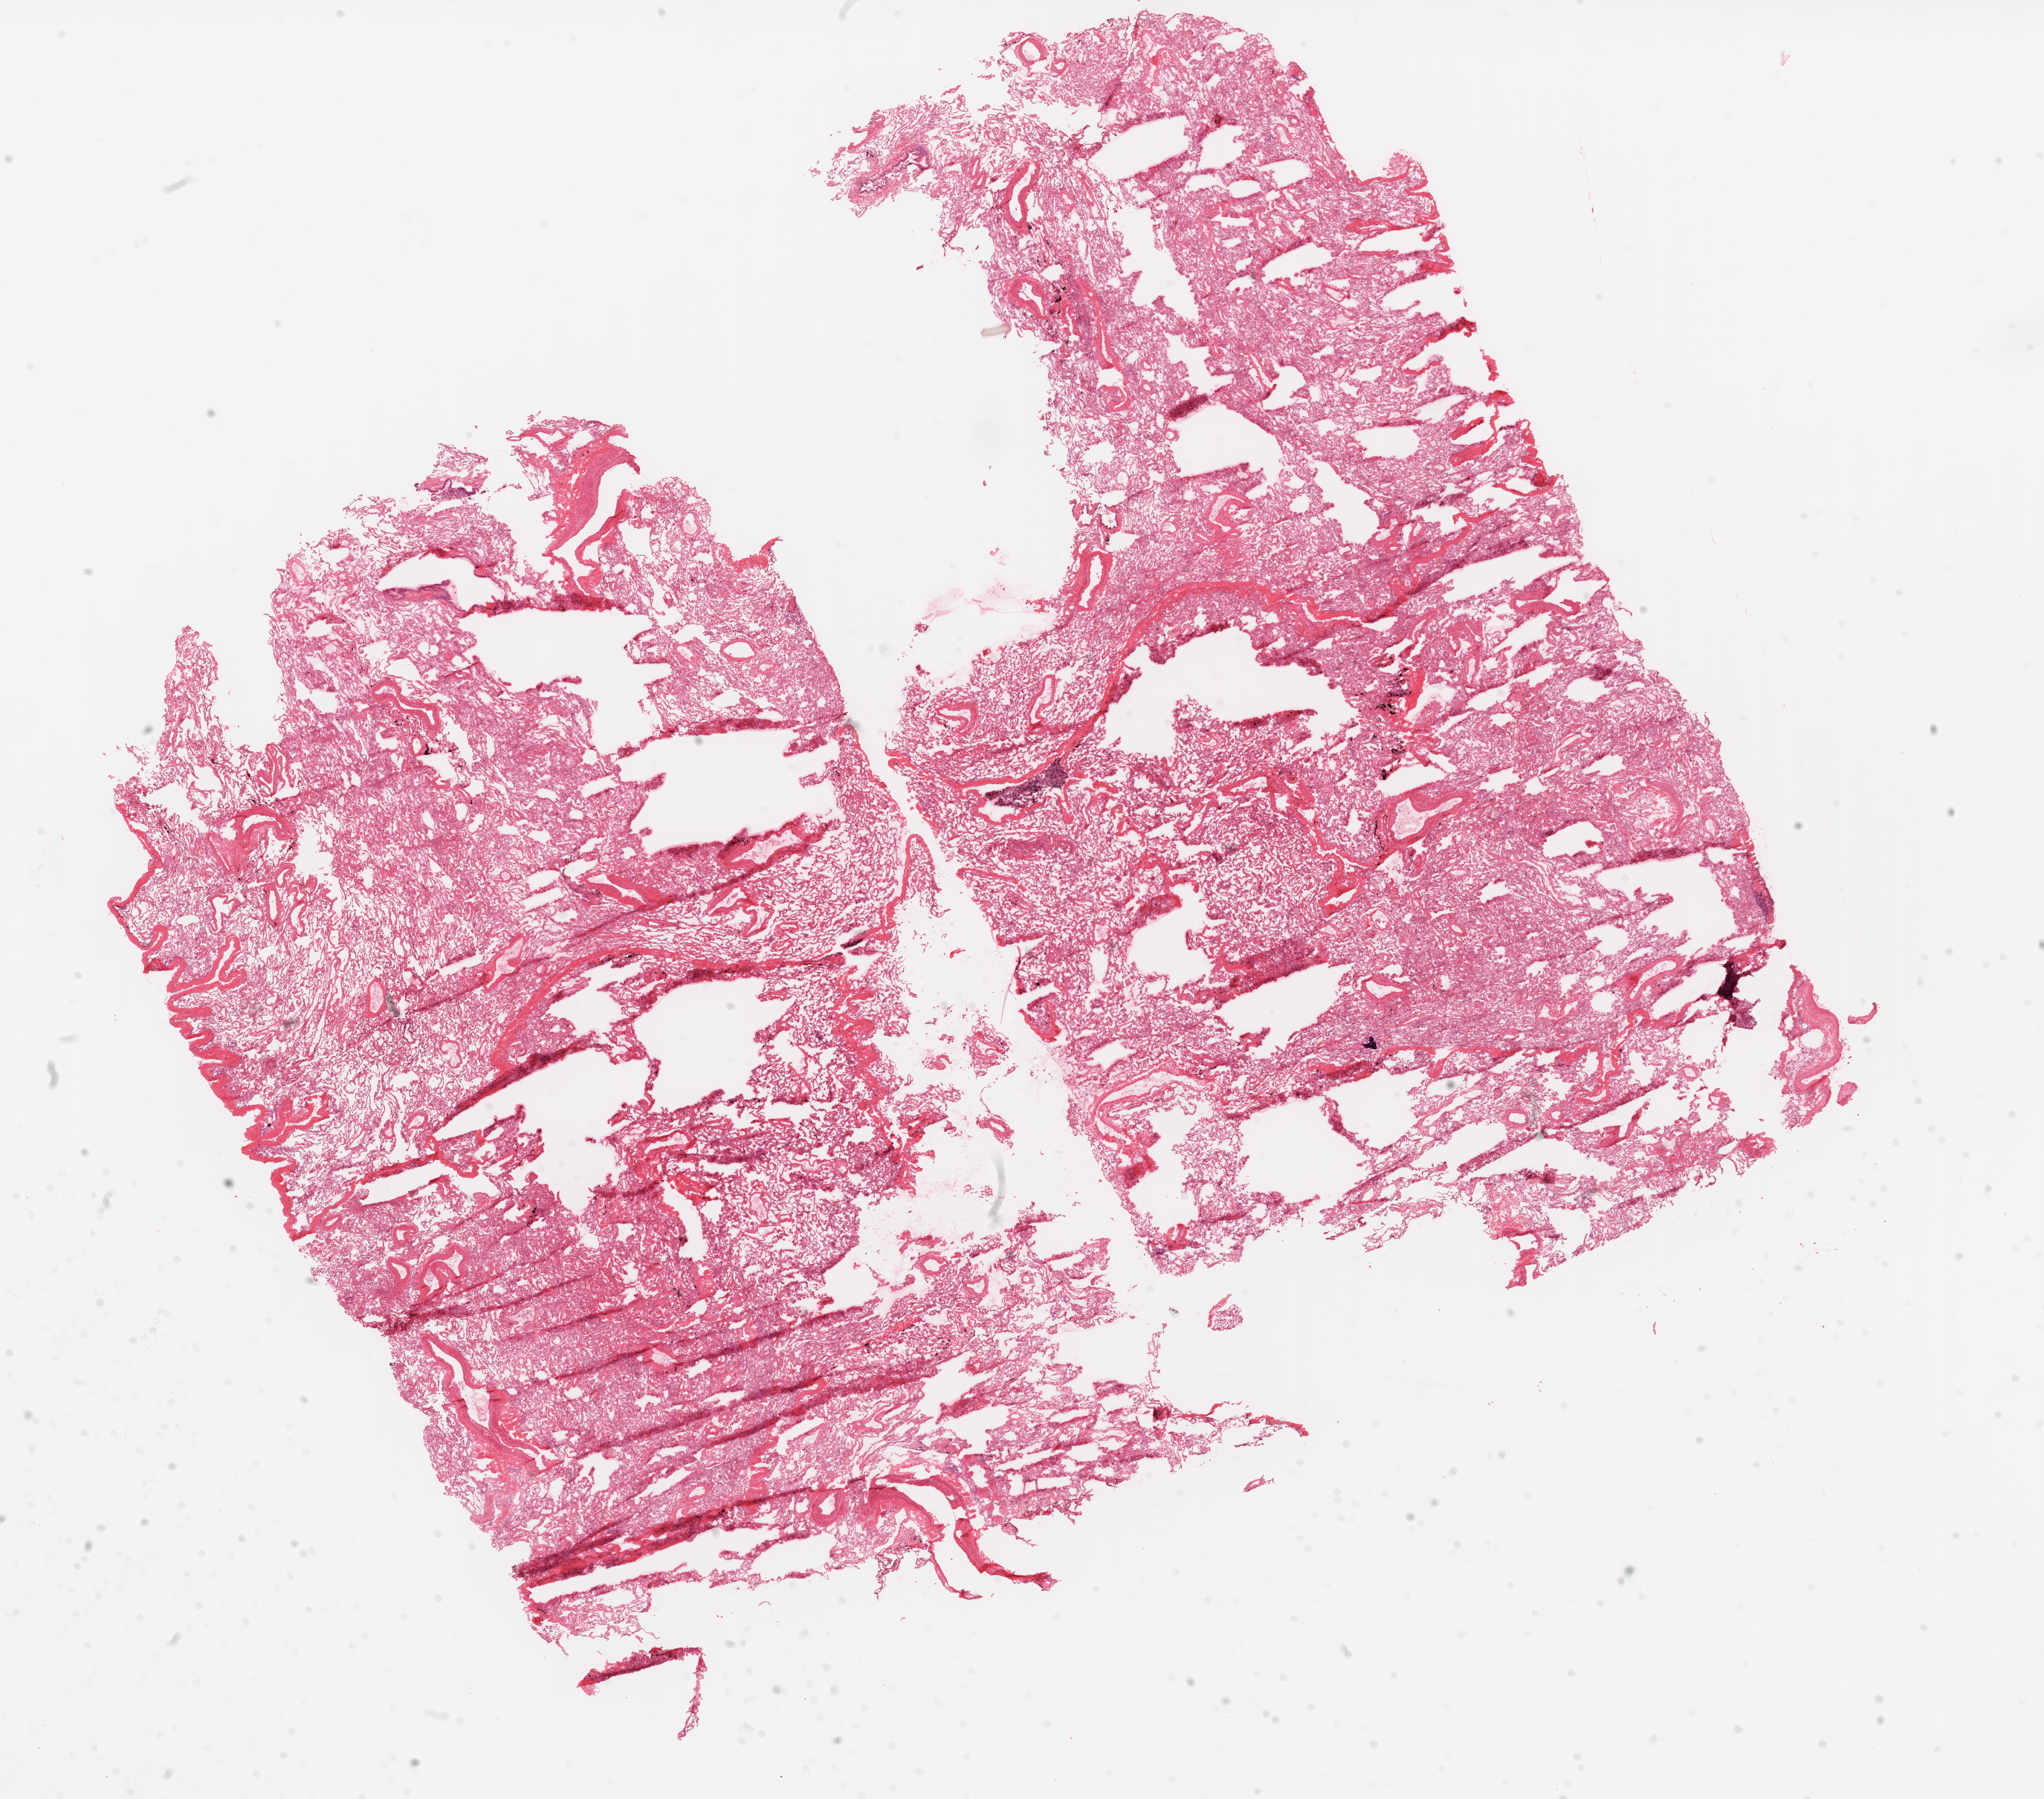
Whole-slide histology image, Hematoxylin and eosin (H&E) stained, a low-resolution overview of the entire scanned area, about 22.1 x 19.4 mm (from a 20x scan), frozen section from the top of the tissue portion, sample: solid tissue normal (non-tumour tissue), lung. Male patient; age at initial diagnosis 73 years.
This section: solid tissue normal sample (biorepository sample class). Patient diagnosis: Squamous cell carcinoma, NOS.